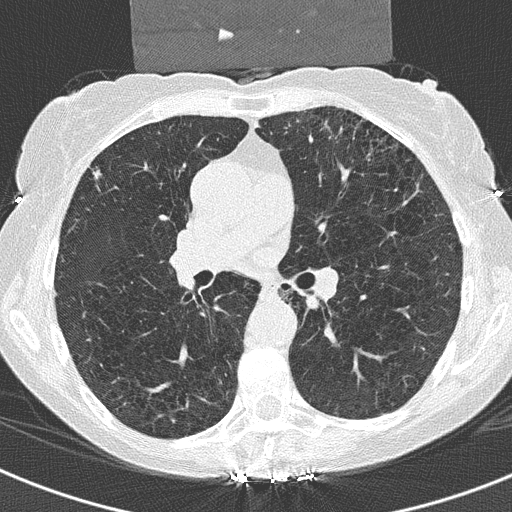
Axial slice from a low-dose chest CT screening exam. Third annual screen. Lung window (W 1500 / L -600 HU). 120 kVp. 512 × 512 image matrix. Female participant, aged 70 years at enrolment. Current smoker at enrolment.
Expert reader's lesion annotation, bounding box (x1, y1, x2, y2) in pixels: (77, 159, 110, 193). Screening reader's record for this exam (one nodule recorded; not confirmed to be the boxed lesion): non-calcified nodule or mass ≥4 mm, right middle lobe, 5 × 5 mm, spiculated (stellate) margins, ground glass attenuation, pre-existing on the prior screen: no. Later outcome: lung cancer diagnosed 321 days after this screen — adenosquamous carcinoma, right upper lobe, poorly differentiated (G3), stage IA (AJCC 6th edition), 12 mm at pathology.